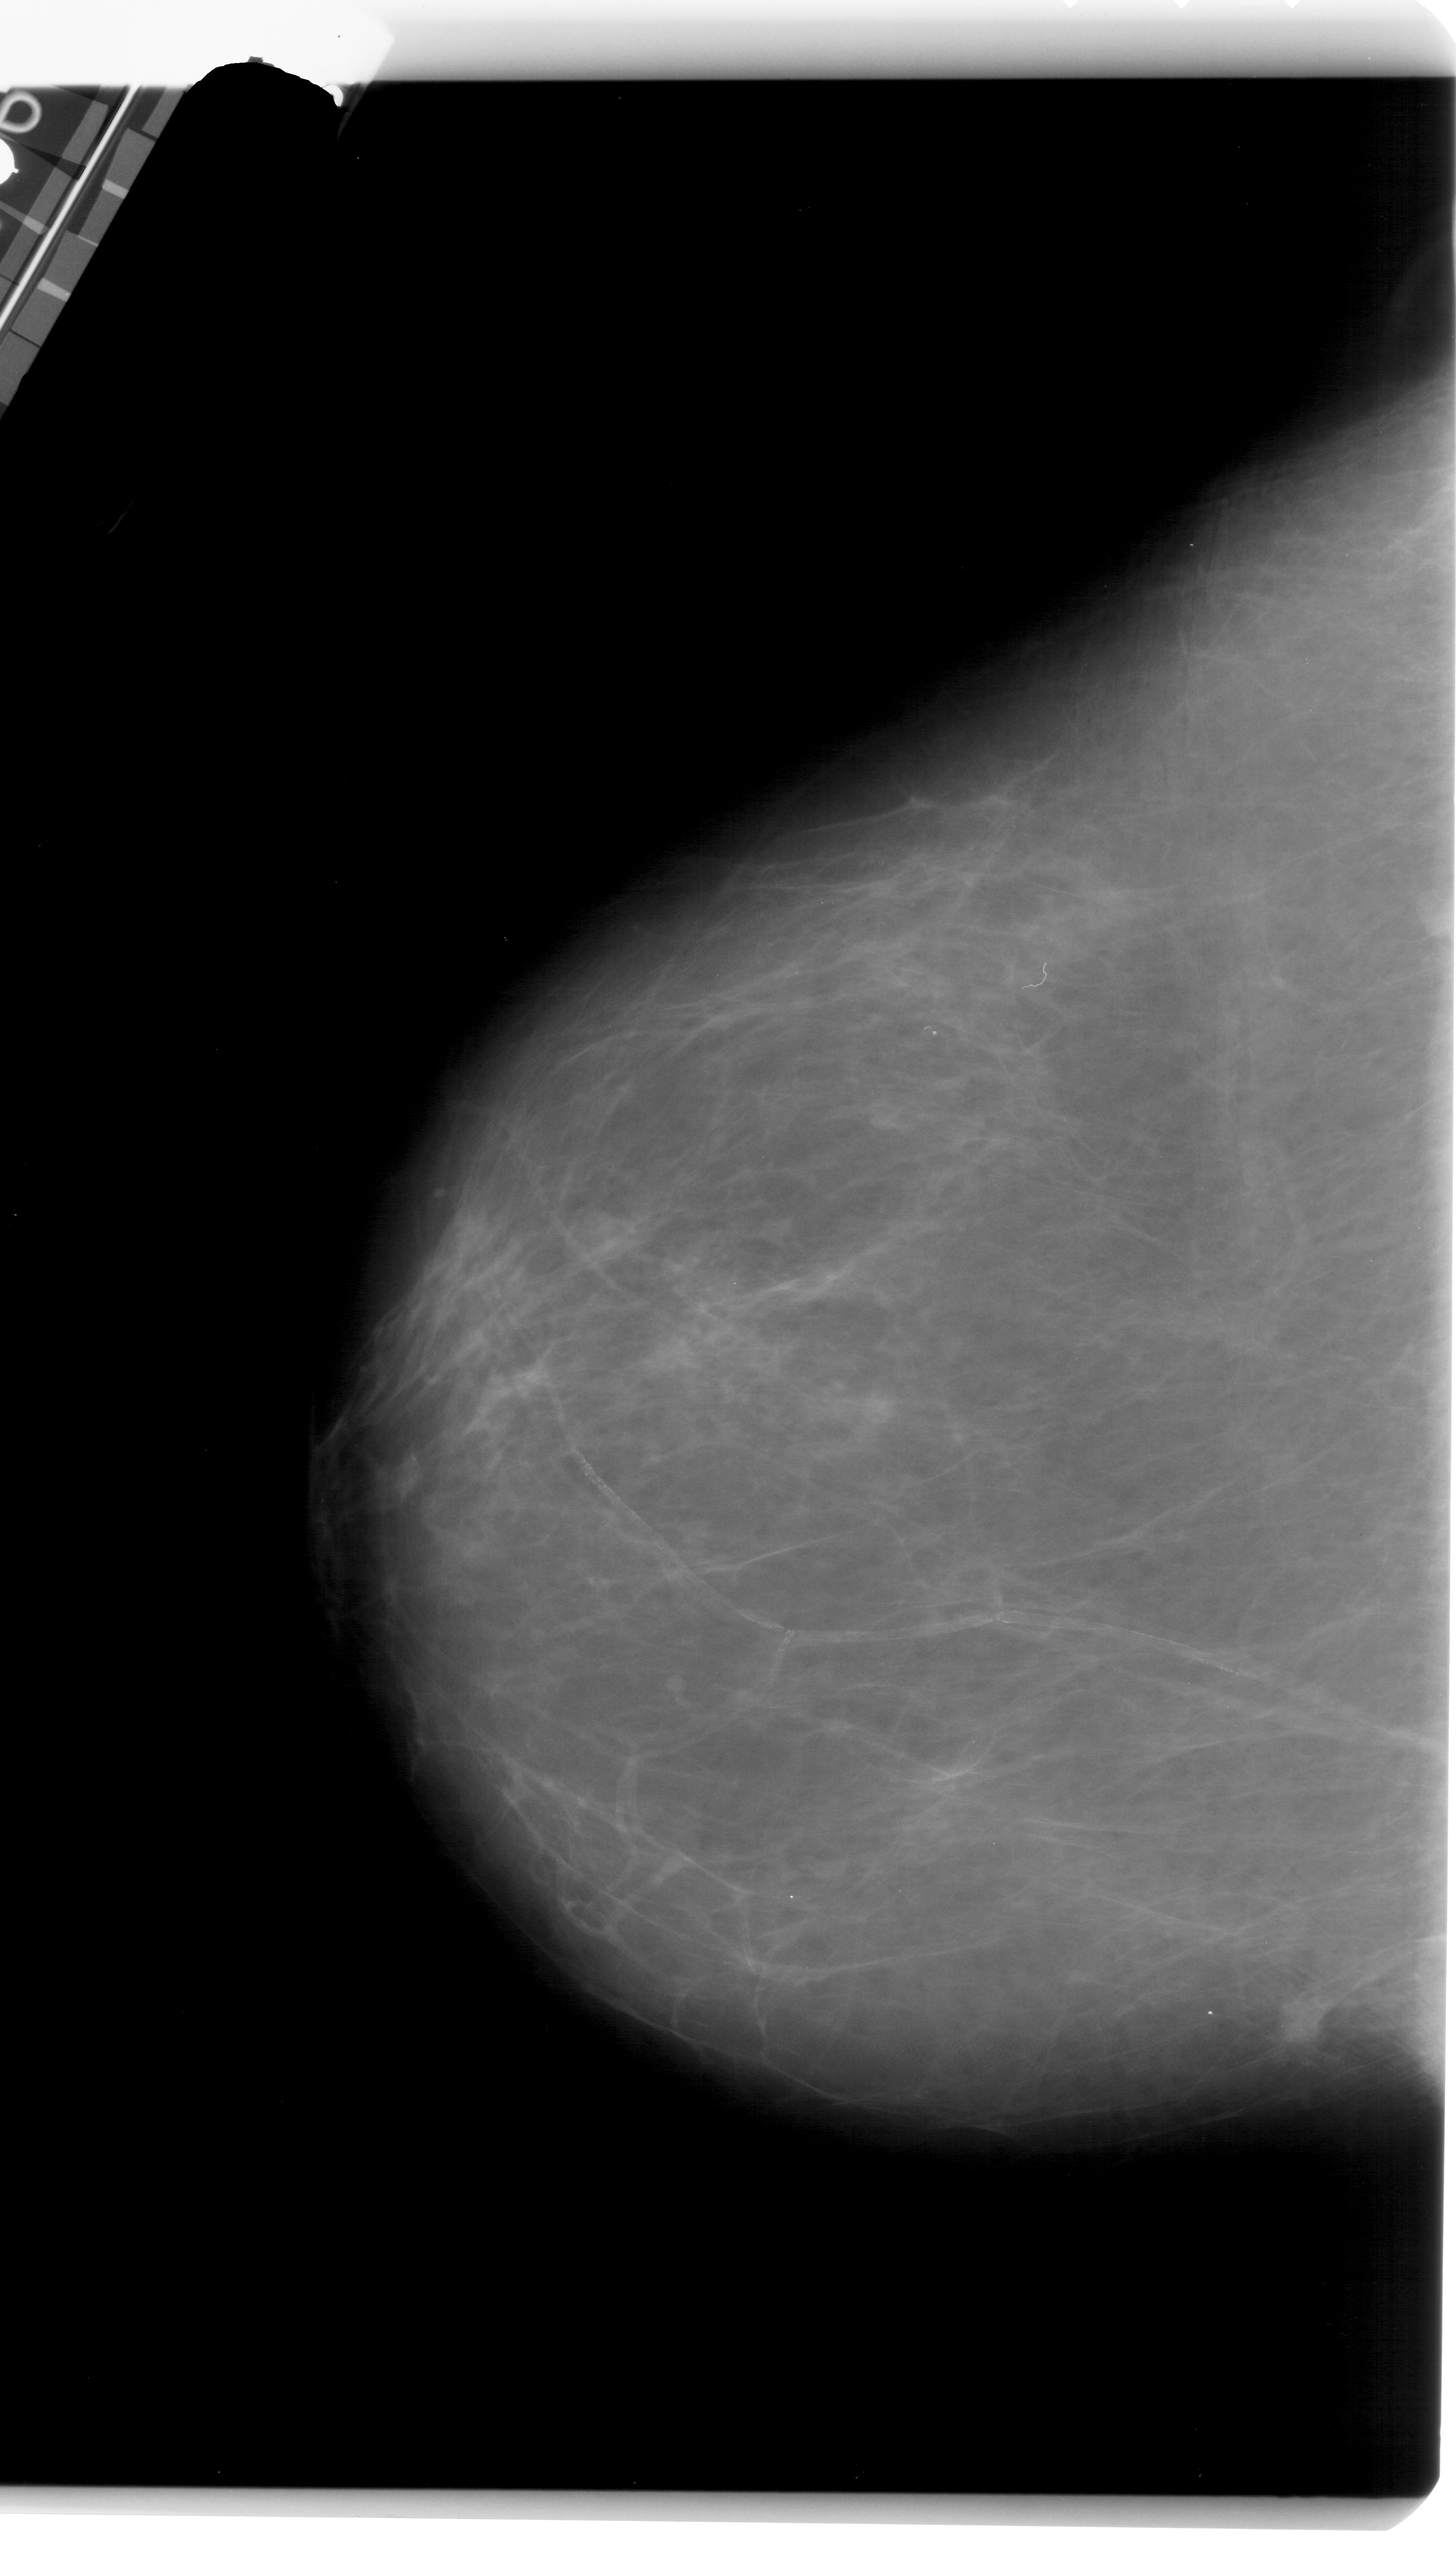
Digitized screen-film mammogram, left breast, craniocaudal (CC) view.
Radiologist-marked abnormalities on this image: mass, shape irregular, margins ill defined; BI-RADS assessment category 4; subtlety rating 2 on a 1 (subtle) to 5 (obvious) scale; pathology (as recorded): malignant.